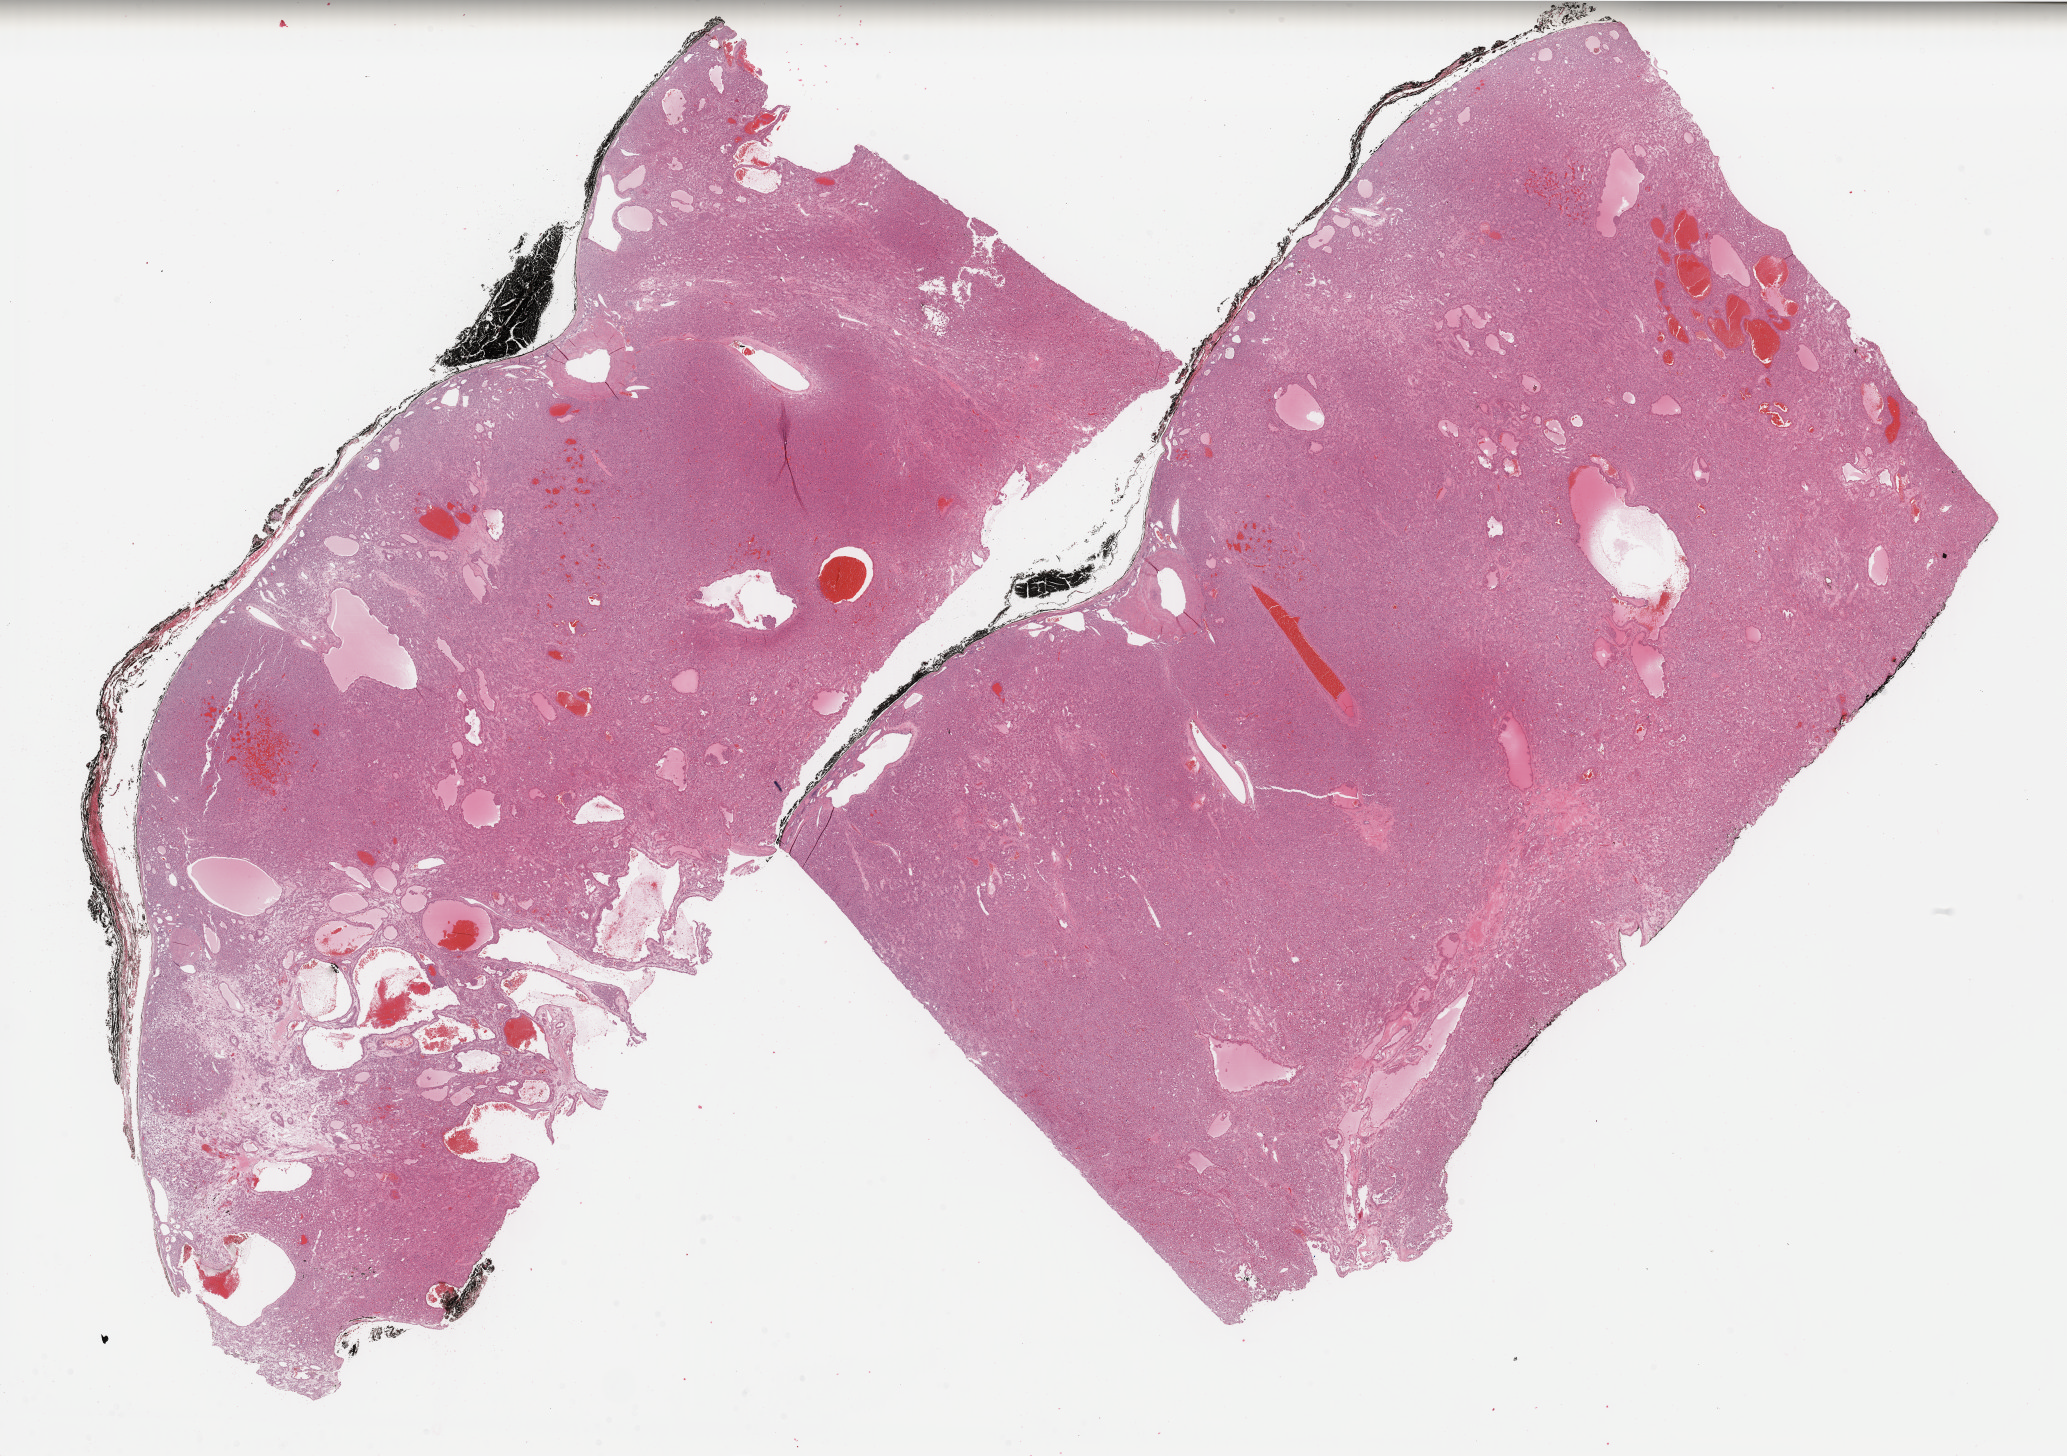
Hematoxylin and eosin (H&E) stained whole-slide image, low-resolution overview of the scanned area, about 32.7 x 23.0 mm, formalin-fixed paraffin-embedded (FFPE) diagnostic section, kidney, primary tumour sample. Female, age 57 years at initial diagnosis. Slide review estimates, as recorded: tumour cells 85%, tumour nuclei 95%, normal cells 0%, stromal cells 10%, necrosis 5%. Inflammatory infiltration, as recorded: lymphocyte infiltration 0%, monocyte infiltration 0%, neutrophil infiltration 0%.
* TNM: T1b N0
* histologic diagnosis: Renal cell carcinoma, chromophobe type
* AJCC pathologic stage: I (7th edition)
* lymph nodes positive (case pathology): 0 of 4 examined